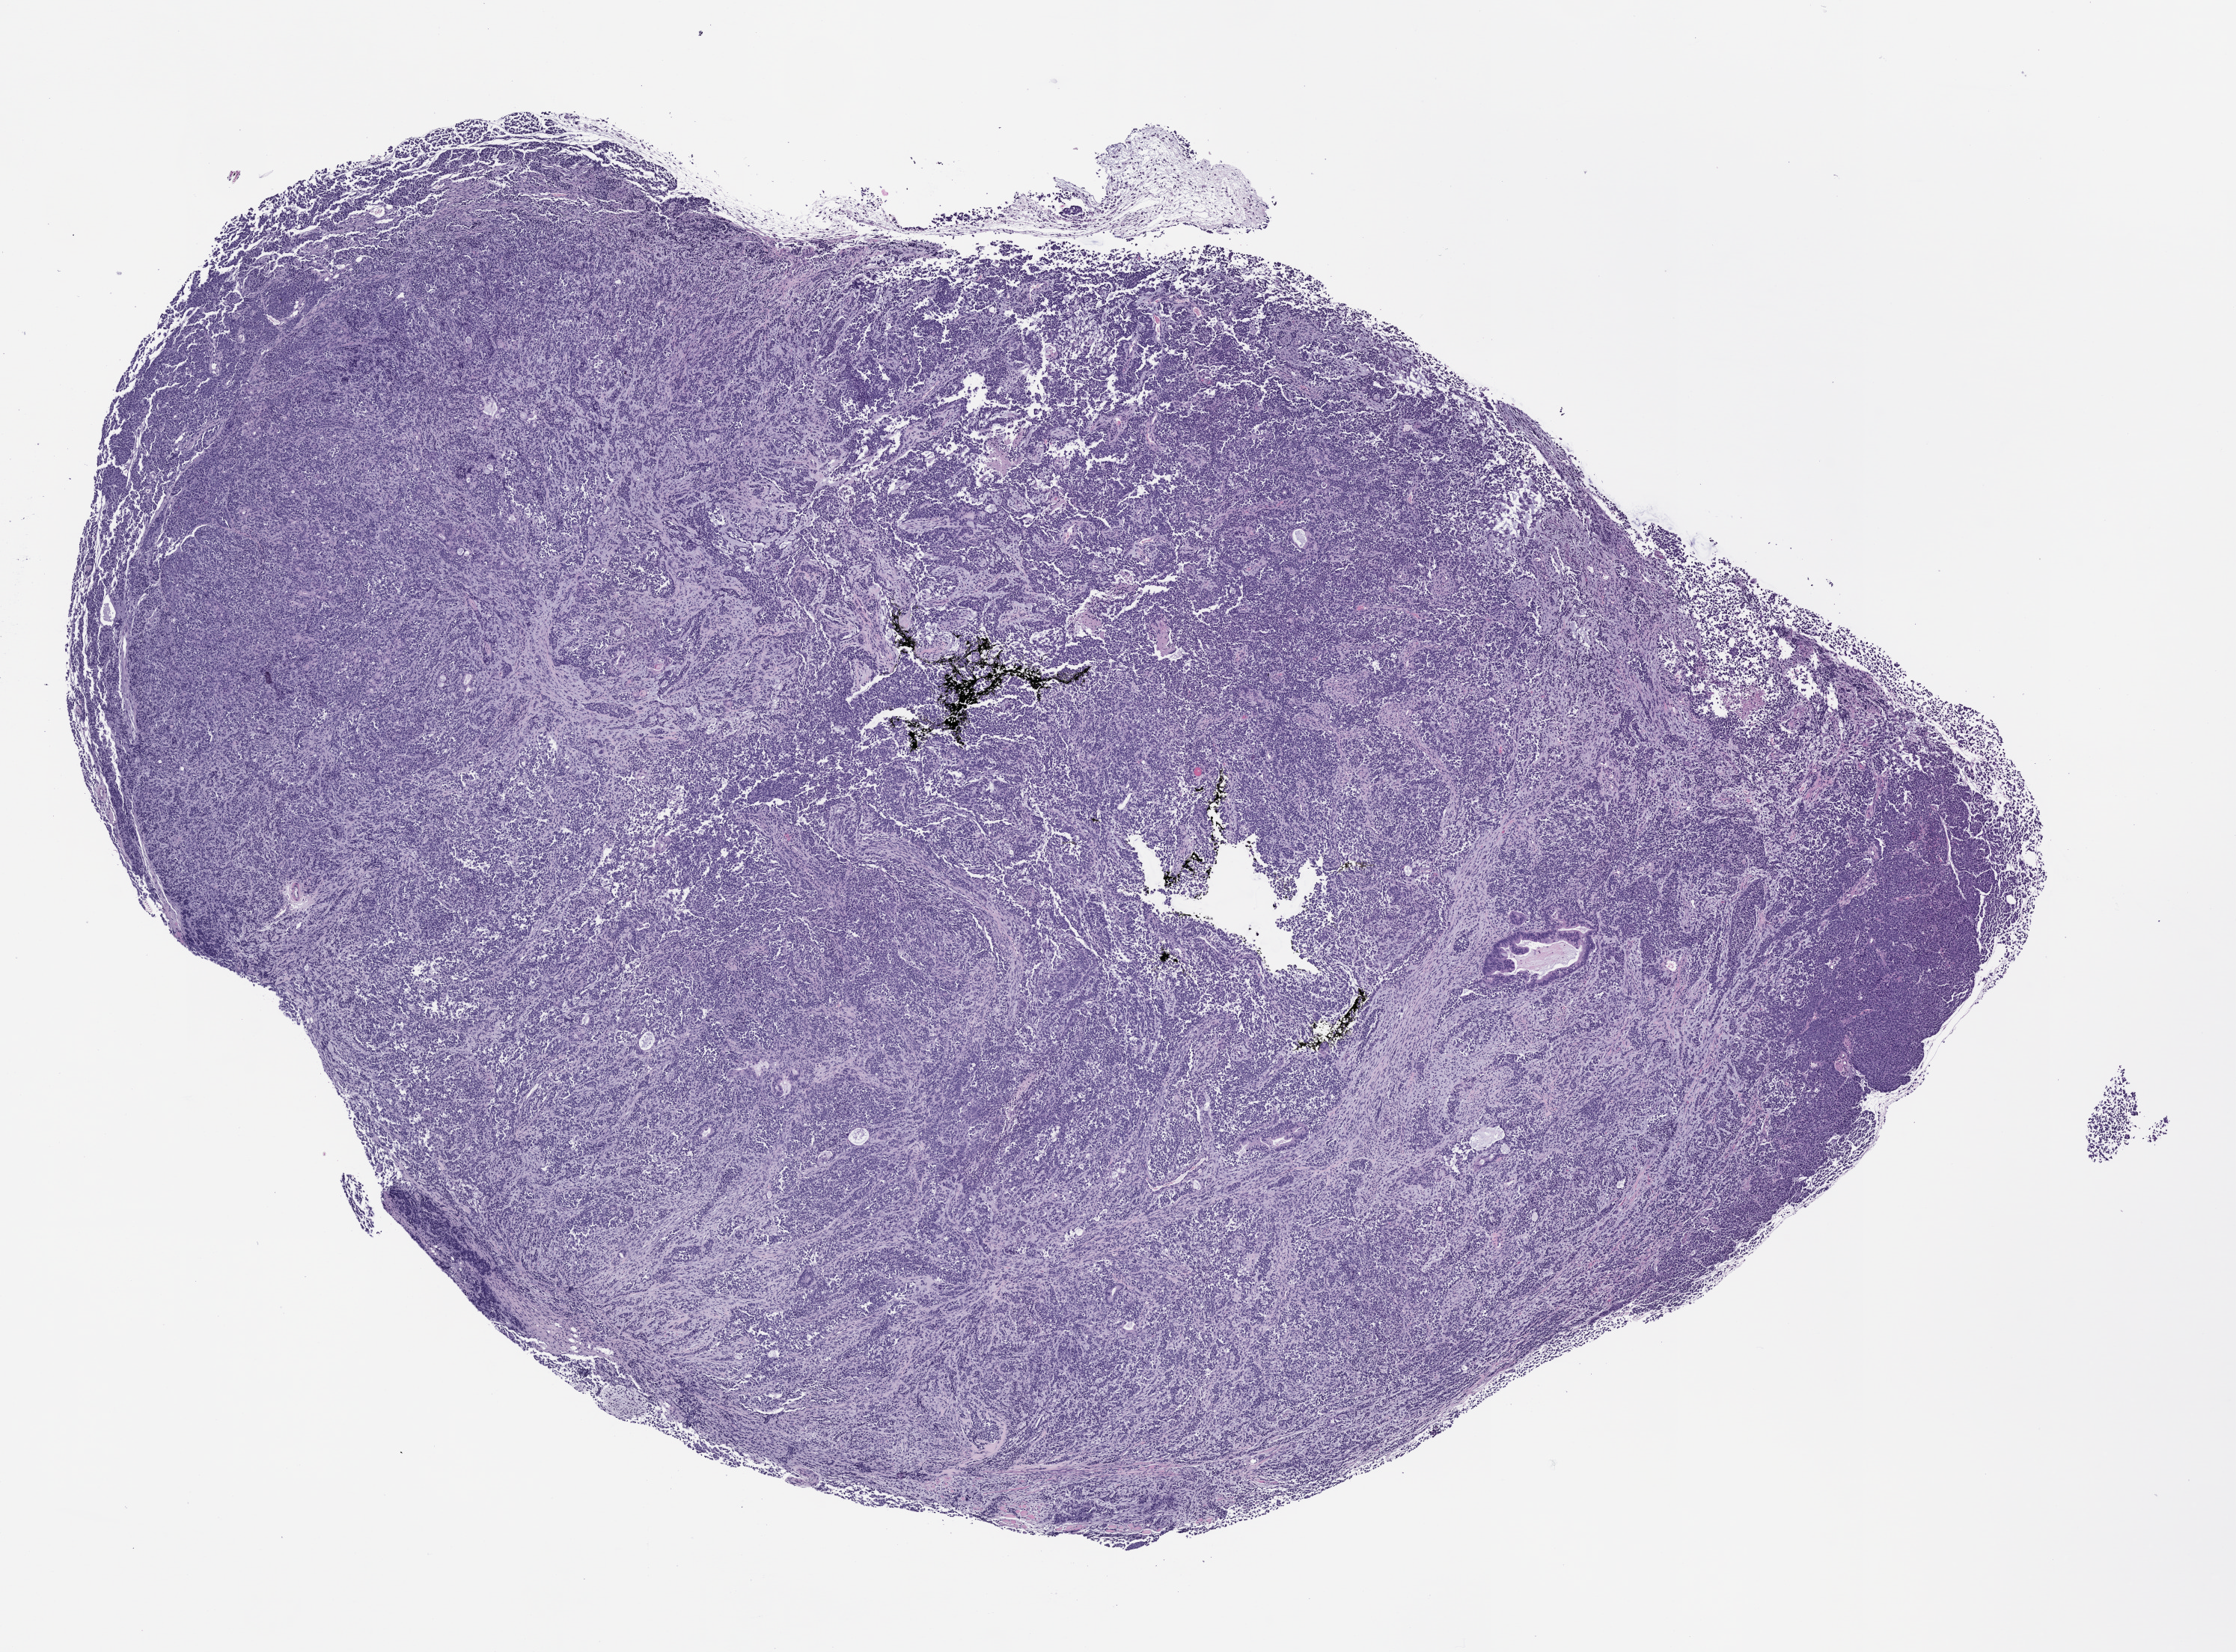
H&E whole-slide image of a patient-derived xenograft (PDX) tumor grown in a mouse, passage 1 — low-resolution overview of the scanned area, about 12.0 x 8.9 mm, formalin-fixed paraffin-embedded section, originating tumor site category: uterus.
Originating patient diagnosis: Carcinosarcoma.